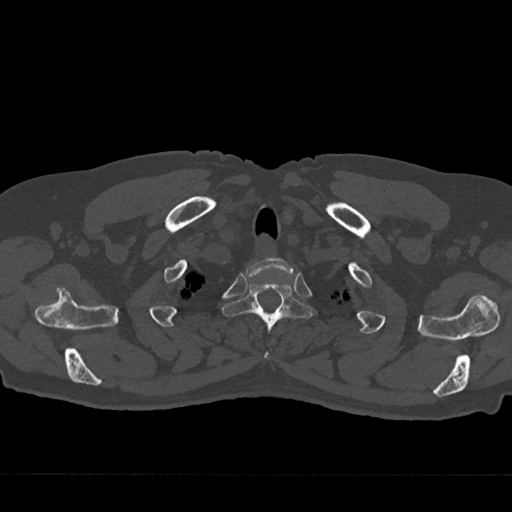
CT including the spine, one axial slice; slice 624 of 797 in the series (ordered by position); 120 kVp; bone window (W 1800 / L 400 HU); 0.5 mm slice thickness; 512 × 512 image matrix, field of view 377 × 377 mm. Patient: male, 75 years. From the clinical record (not read from this slice): primary cancer: renal.
Outlined on this slice (semi-automatically segmented with operator editing):
- T1 vertebra: bounding box <245,258,294,279> (left, top, right, bottom; pixels)
- T2 vertebra: <221,282,316,359>